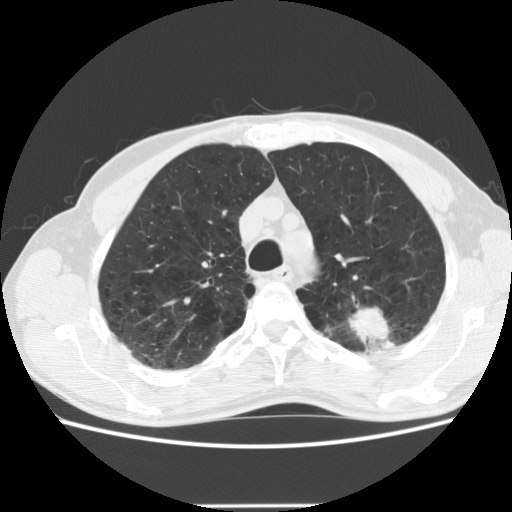
Low-dose screening chest CT, one axial slice. Position 148 of 191 along the scan axis. Reconstruction kernel STANDARD. Lung window (W 1500 / L -600 HU). 2.5 mm slice thickness. 512 × 512 image matrix, field of view 352 × 352 mm.
Annotated regions visible in this slice (manually delineated by an expert):
- lesion 1 (tumor, upper lobe of left lung): bounding box <350,307,389,342> (left, top, right, bottom; pixels)